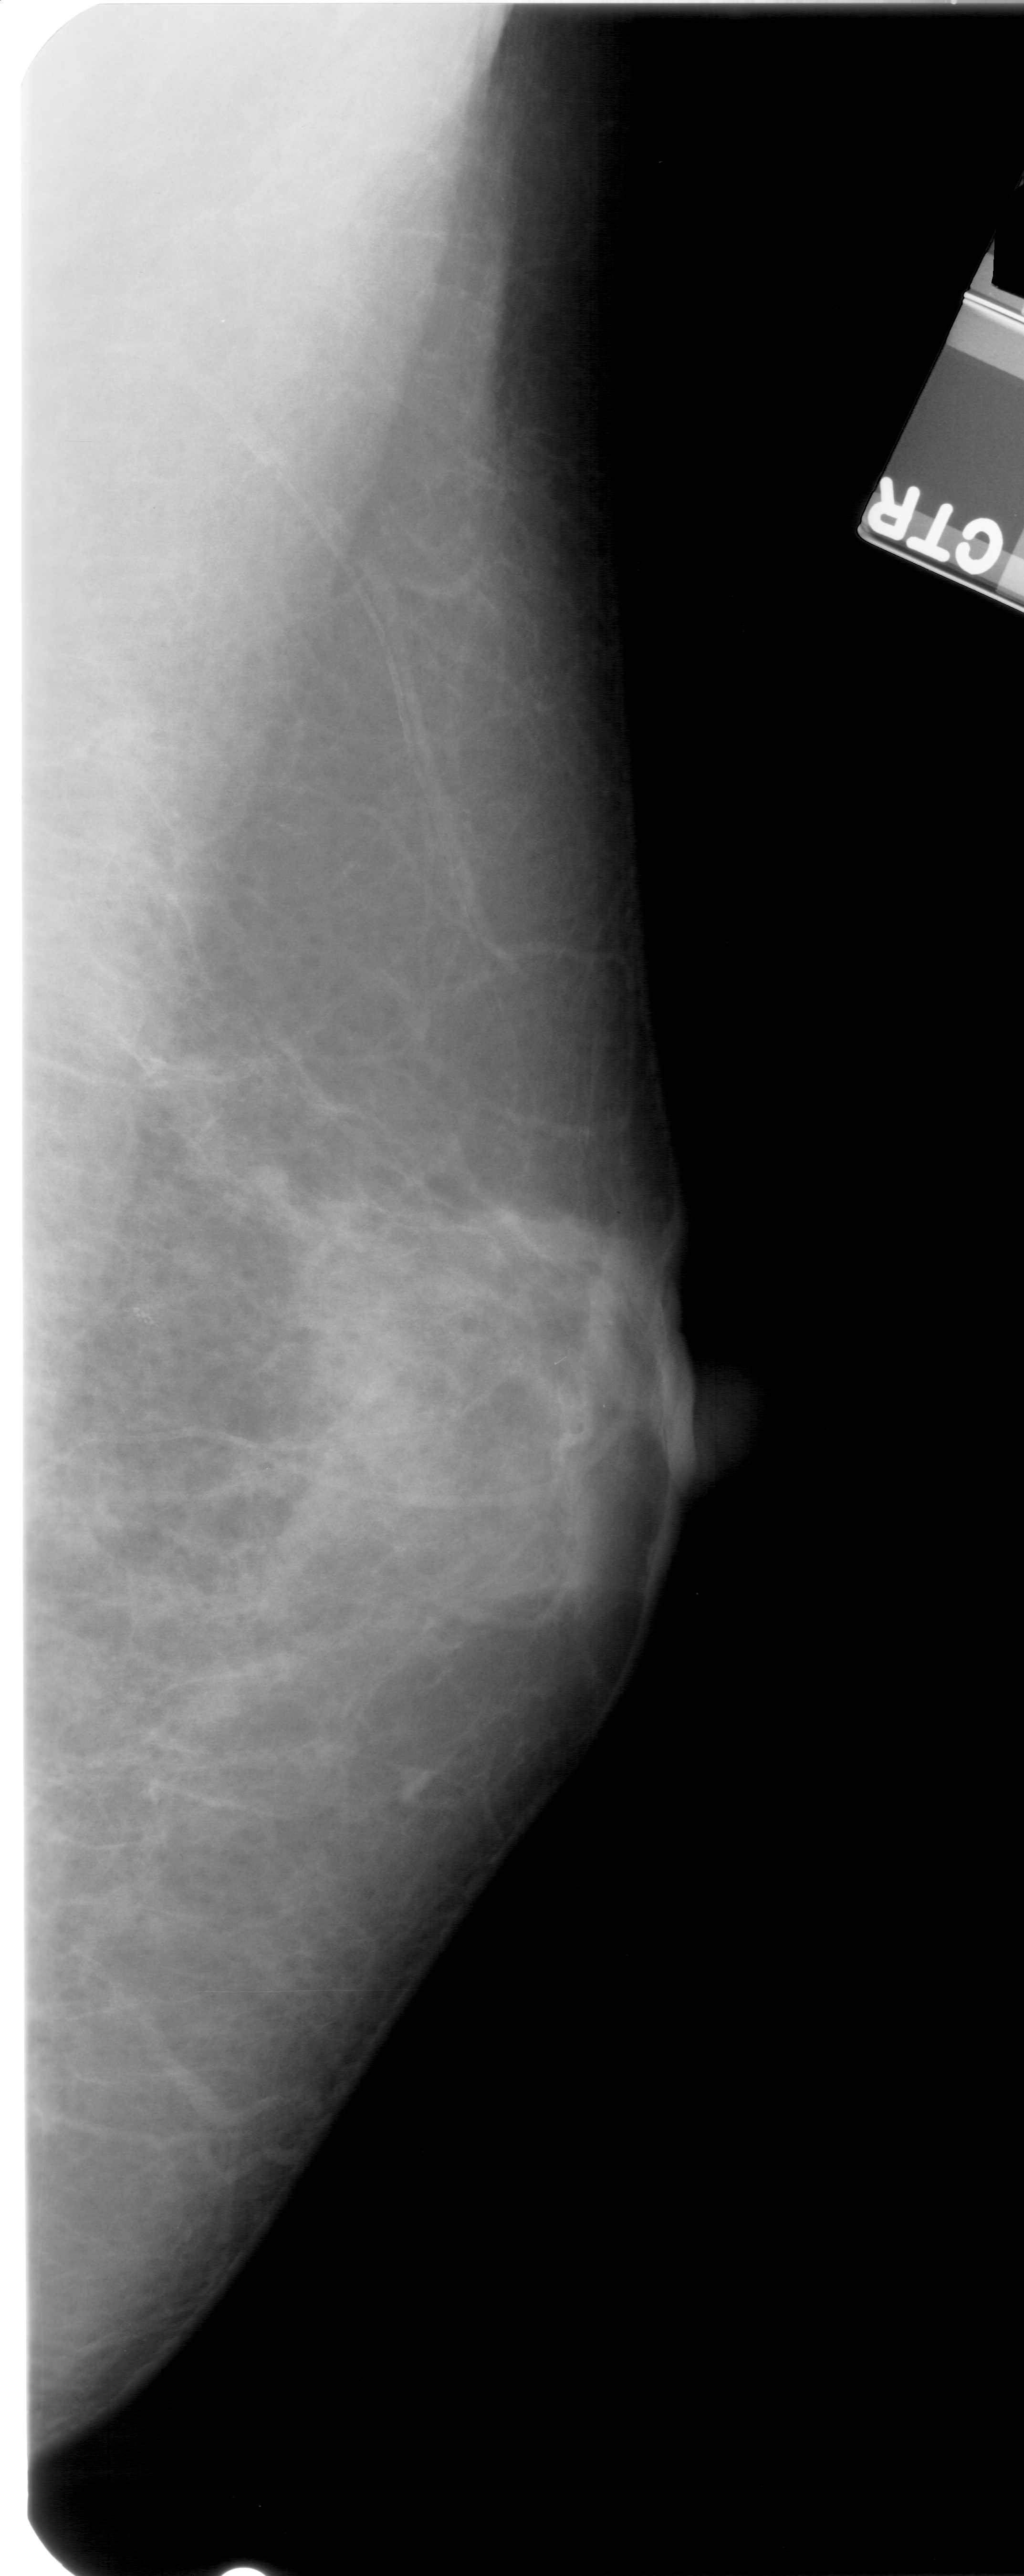
Mammogram (digitized film), right breast, mediolateral oblique (MLO) view, breast composition: extremely dense (BI-RADS density category 4 of 4).
Abnormality record for this image: calcifications, morphology pleomorphic, distribution clustered; BI-RADS assessment category 4; subtlety rating 4 on a 1 (subtle) to 5 (obvious) scale; pathology (as recorded): benign.